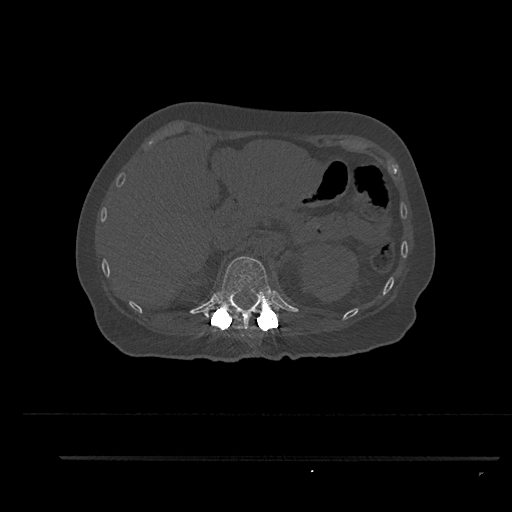
CT including the spine, one axial slice; slice 264 of 797 in the series (ordered by position); reconstruction kernel Br40s/3; 120 kVp; bone window (W 1800 / L 400 HU); 0.5 mm slice thickness; 512 × 512 image matrix, field of view 408 × 408 mm. Patient: female, 44 years. From the clinical record (not read from this slice): primary cancer: renal; vertebrae with lytic lesions (as recorded): L1.
Annotated regions visible in this slice (semi-automatic segmentation, software-assisted and operator-edited):
- T12 vertebra: bounding box <205,256,281,331> (left, top, right, bottom; pixels)